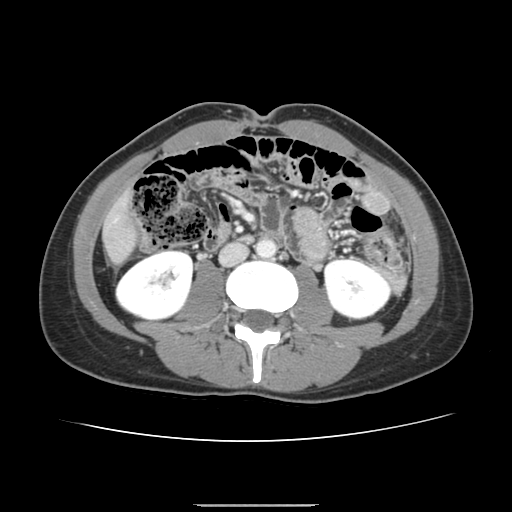
Contrast-enhanced abdominal CT, one axial slice. Position 38 of 150 along the scan axis. 120 kVp. Intravenous contrast given. Soft-tissue window (W 400 / L 40 HU). 512 × 512 image matrix, field of view 324 × 324 mm. Female patient, age 32 years. Case-level facts recorded for this patient, not image findings: diagnosis: colorectal cancer liver metastases, imaged before liver resection; multiple liver metastases: yes; largest metastasis: 0.7 cm.
Structures marked on this image (outlined manually by an expert reader):
- liver: bounding box <105,199,134,261> (left, top, right, bottom; pixels)
- planned liver remnant (the part of the liver to remain after resection): <105,200,134,261>